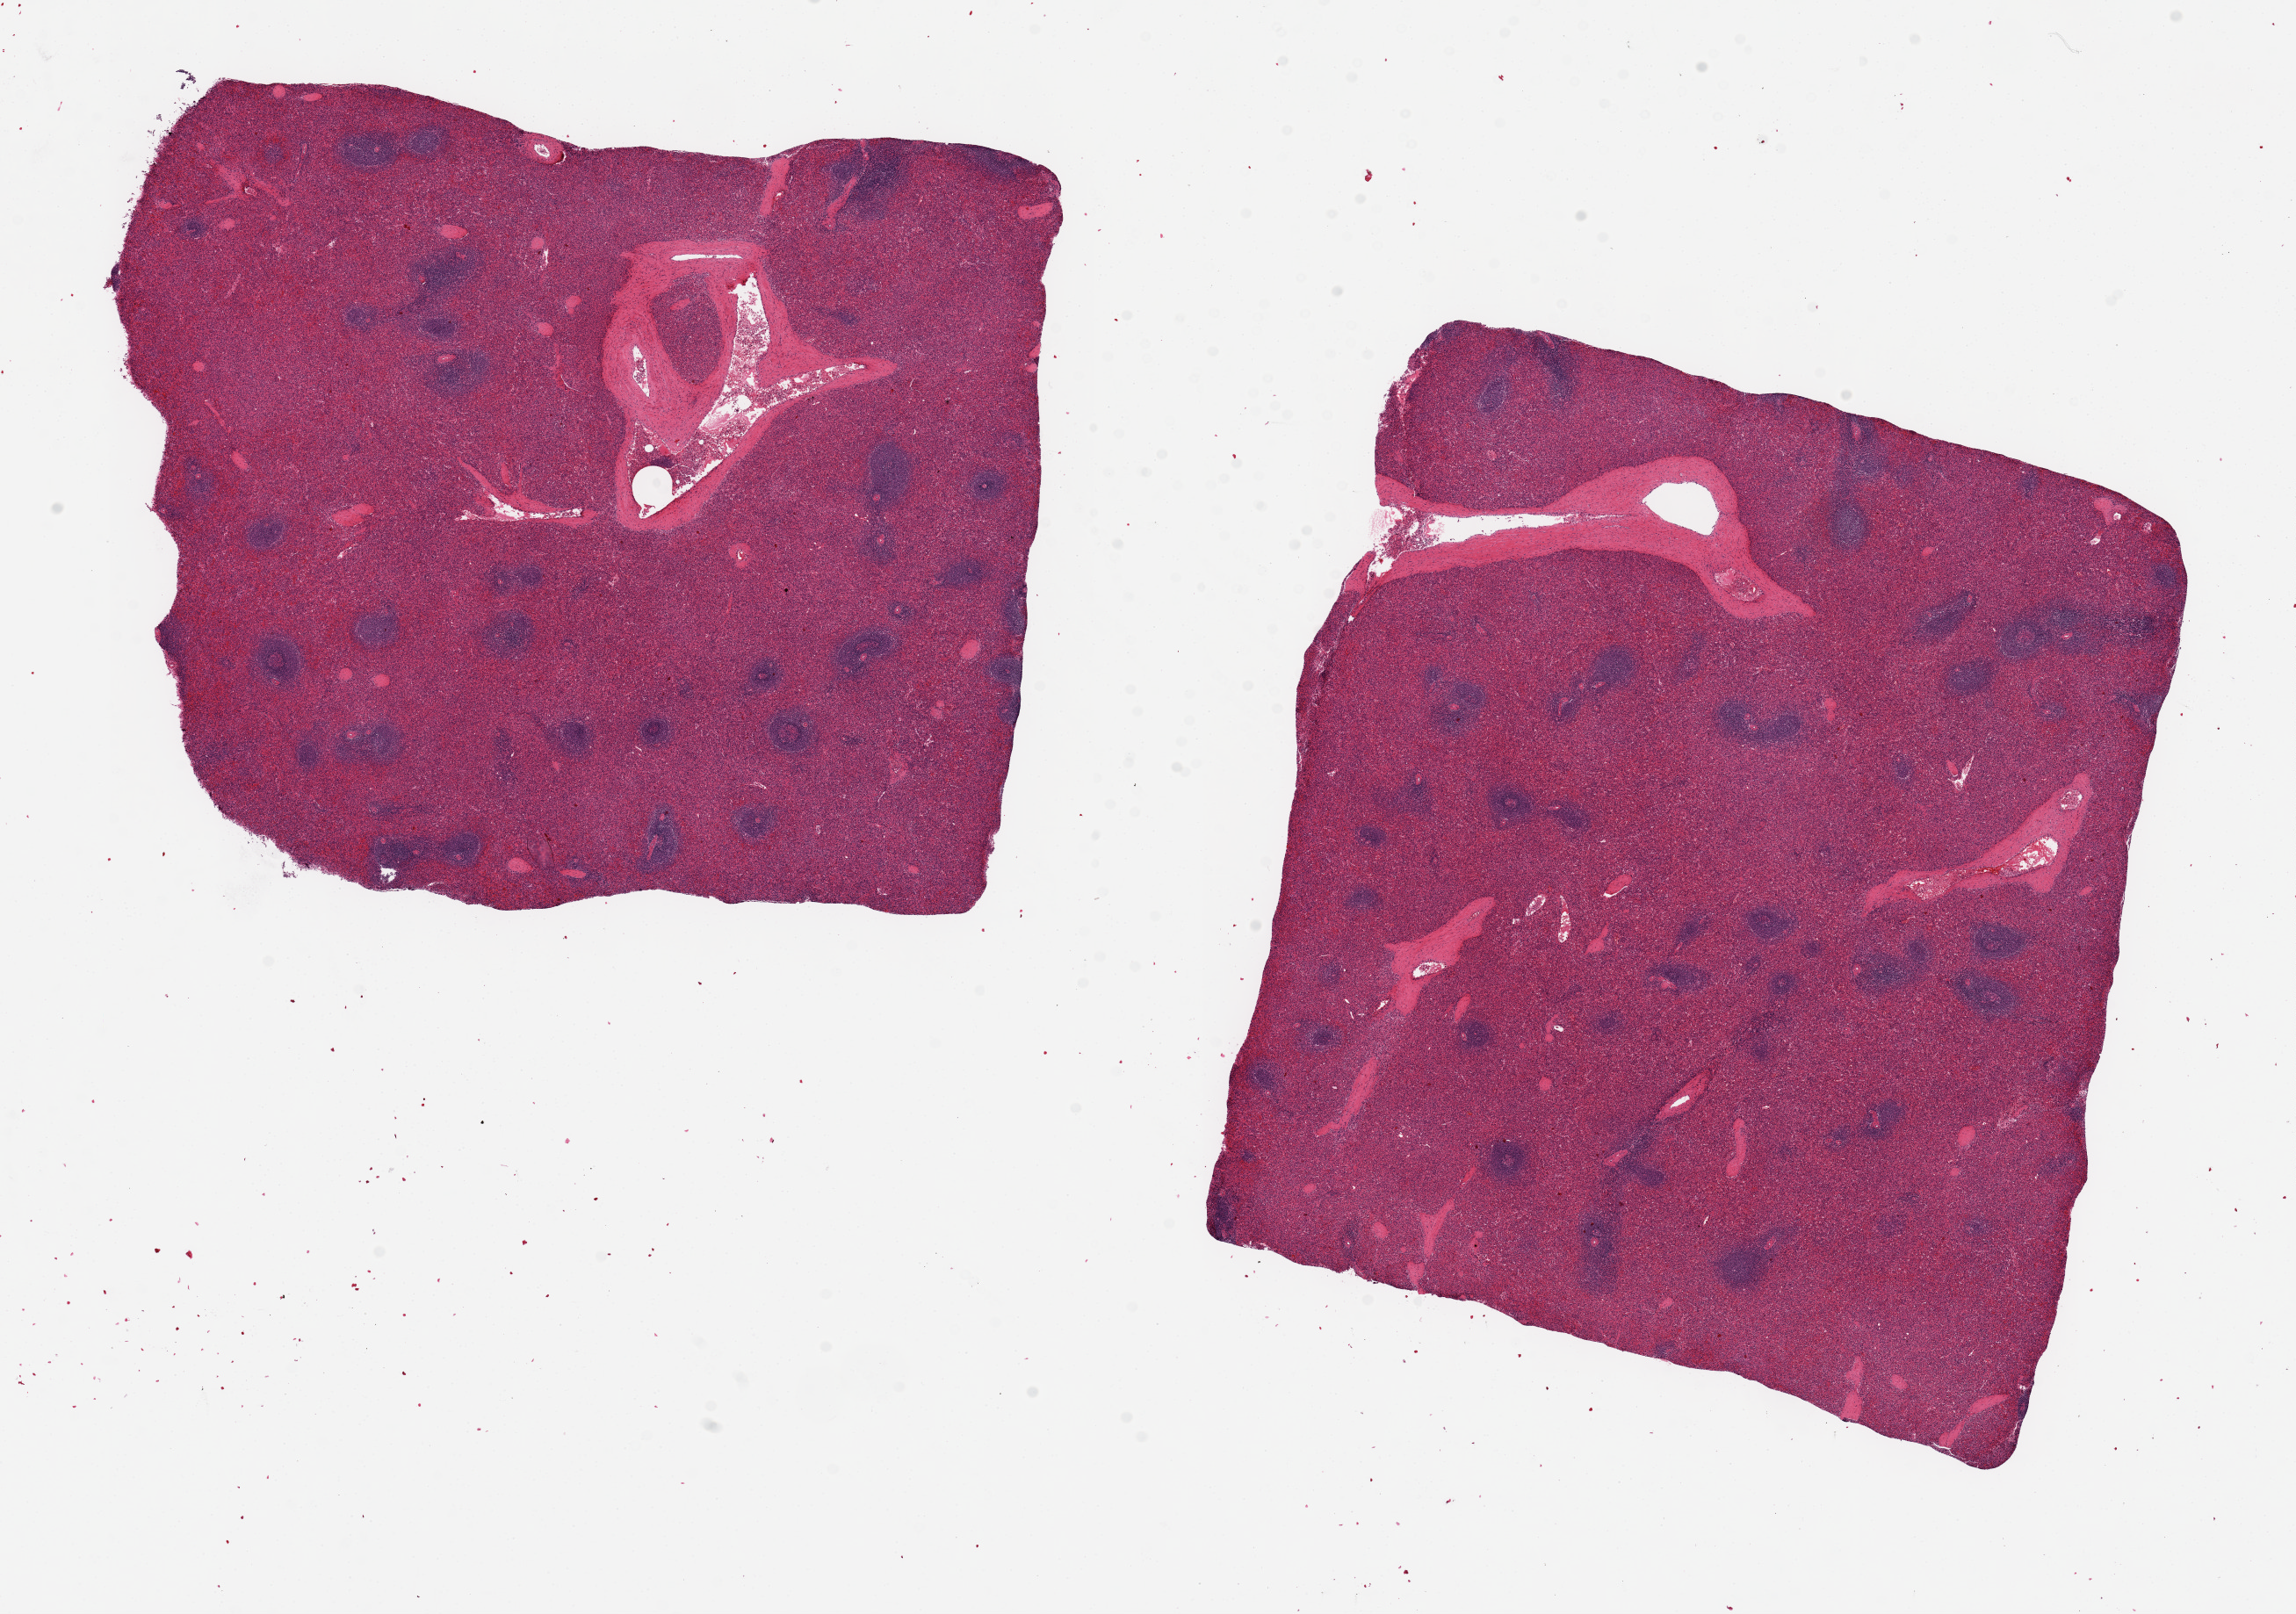
Digitized hematoxylin and eosin (H&E)-stained section, shown as a low-resolution overview of the whole scanned area (about 20.7 x 14.5 mm, acquisition: 20x scan). PAXgene-fixed, paraffin-embedded tissue. Section of spleen (target tissue). Tissue donor sample. Donor: male.
Reviewer comment on this tissue sample: 2 pieces ~8x7 mm; not congested.